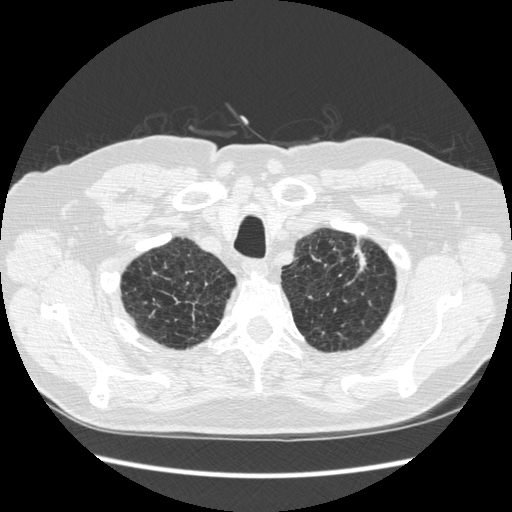
Low-dose screening chest CT, one axial slice. Position 238 of 267 along the scan axis. Reconstruction kernel STANDARD. 120 kVp. Lung window (W 1500 / L -600 HU). 1.25 mm slice thickness. 512 × 512 image matrix, field of view 360 × 360 mm.
Outlined on this slice (outlined manually by an expert reader):
- lesion 1 (tumor, upper lobe of left lung): bounding box [x1, y1, x2, y2] px = [354, 250, 366, 271]